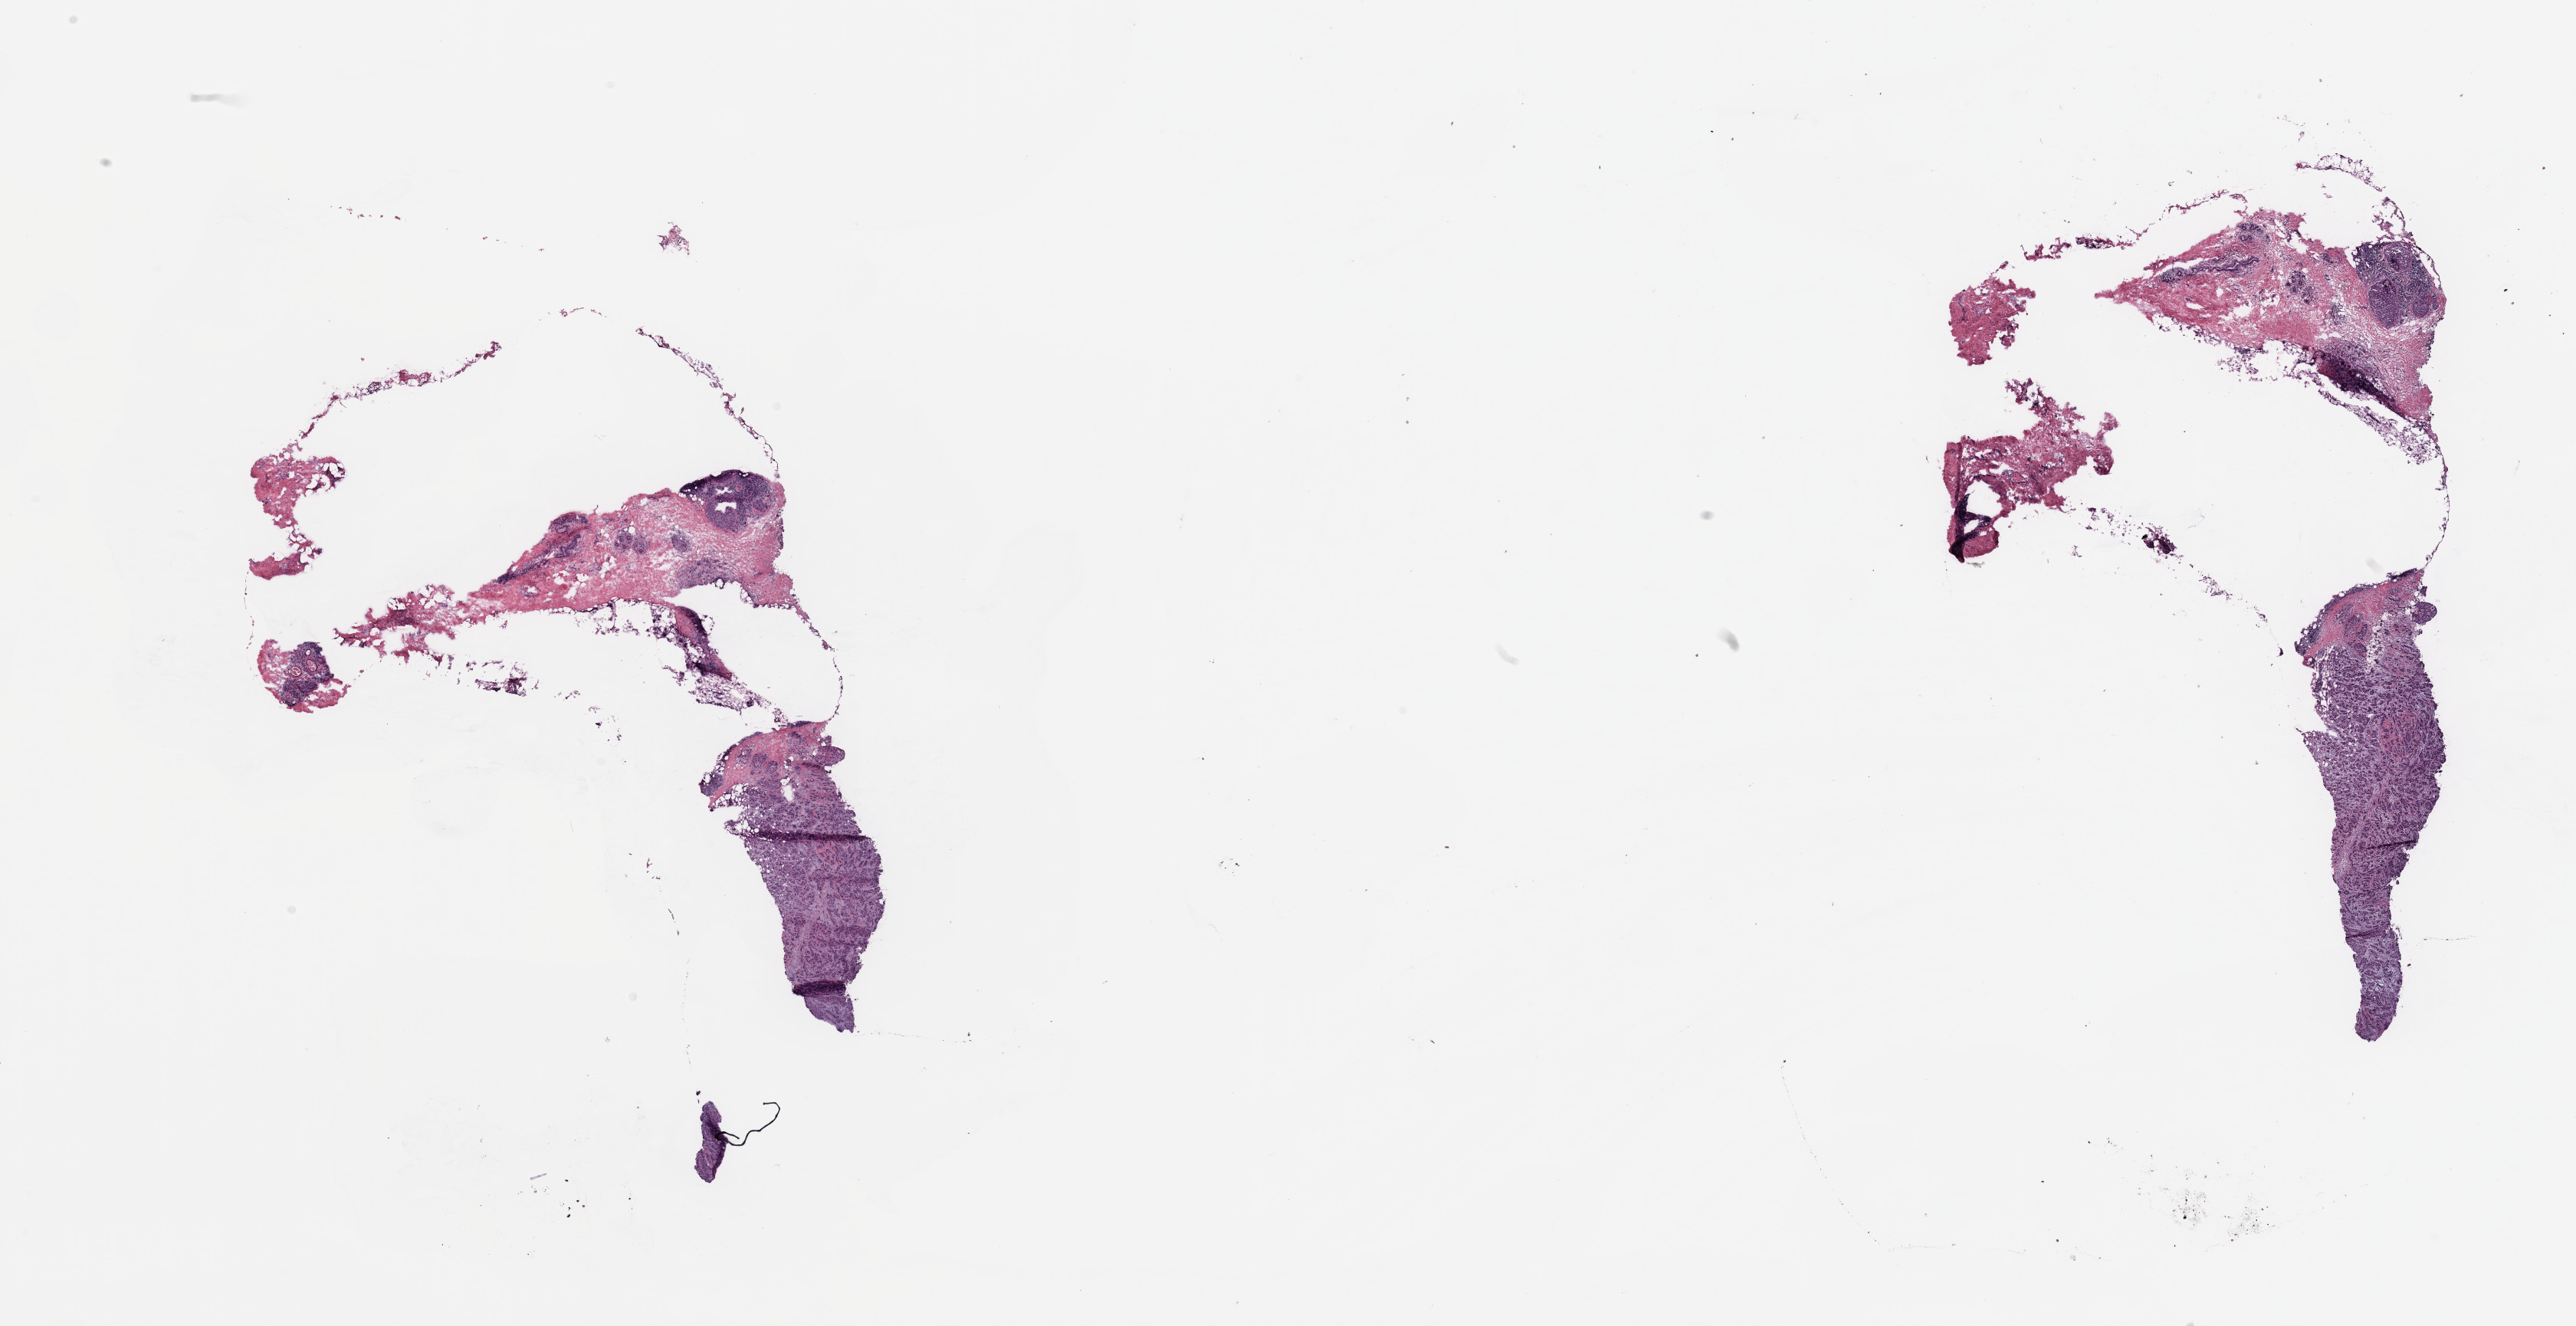
Digitized H&E tissue section (whole slide), whole scanned area (about 26.6 x 13.7 mm, slide scanned at 20x) shown as a low-resolution overview; breast, tumour tissue. Female, 52 y/o.
Histologic diagnosis: Infiltrating duct carcinoma, NOS. AJCC pathologic stage: IA.